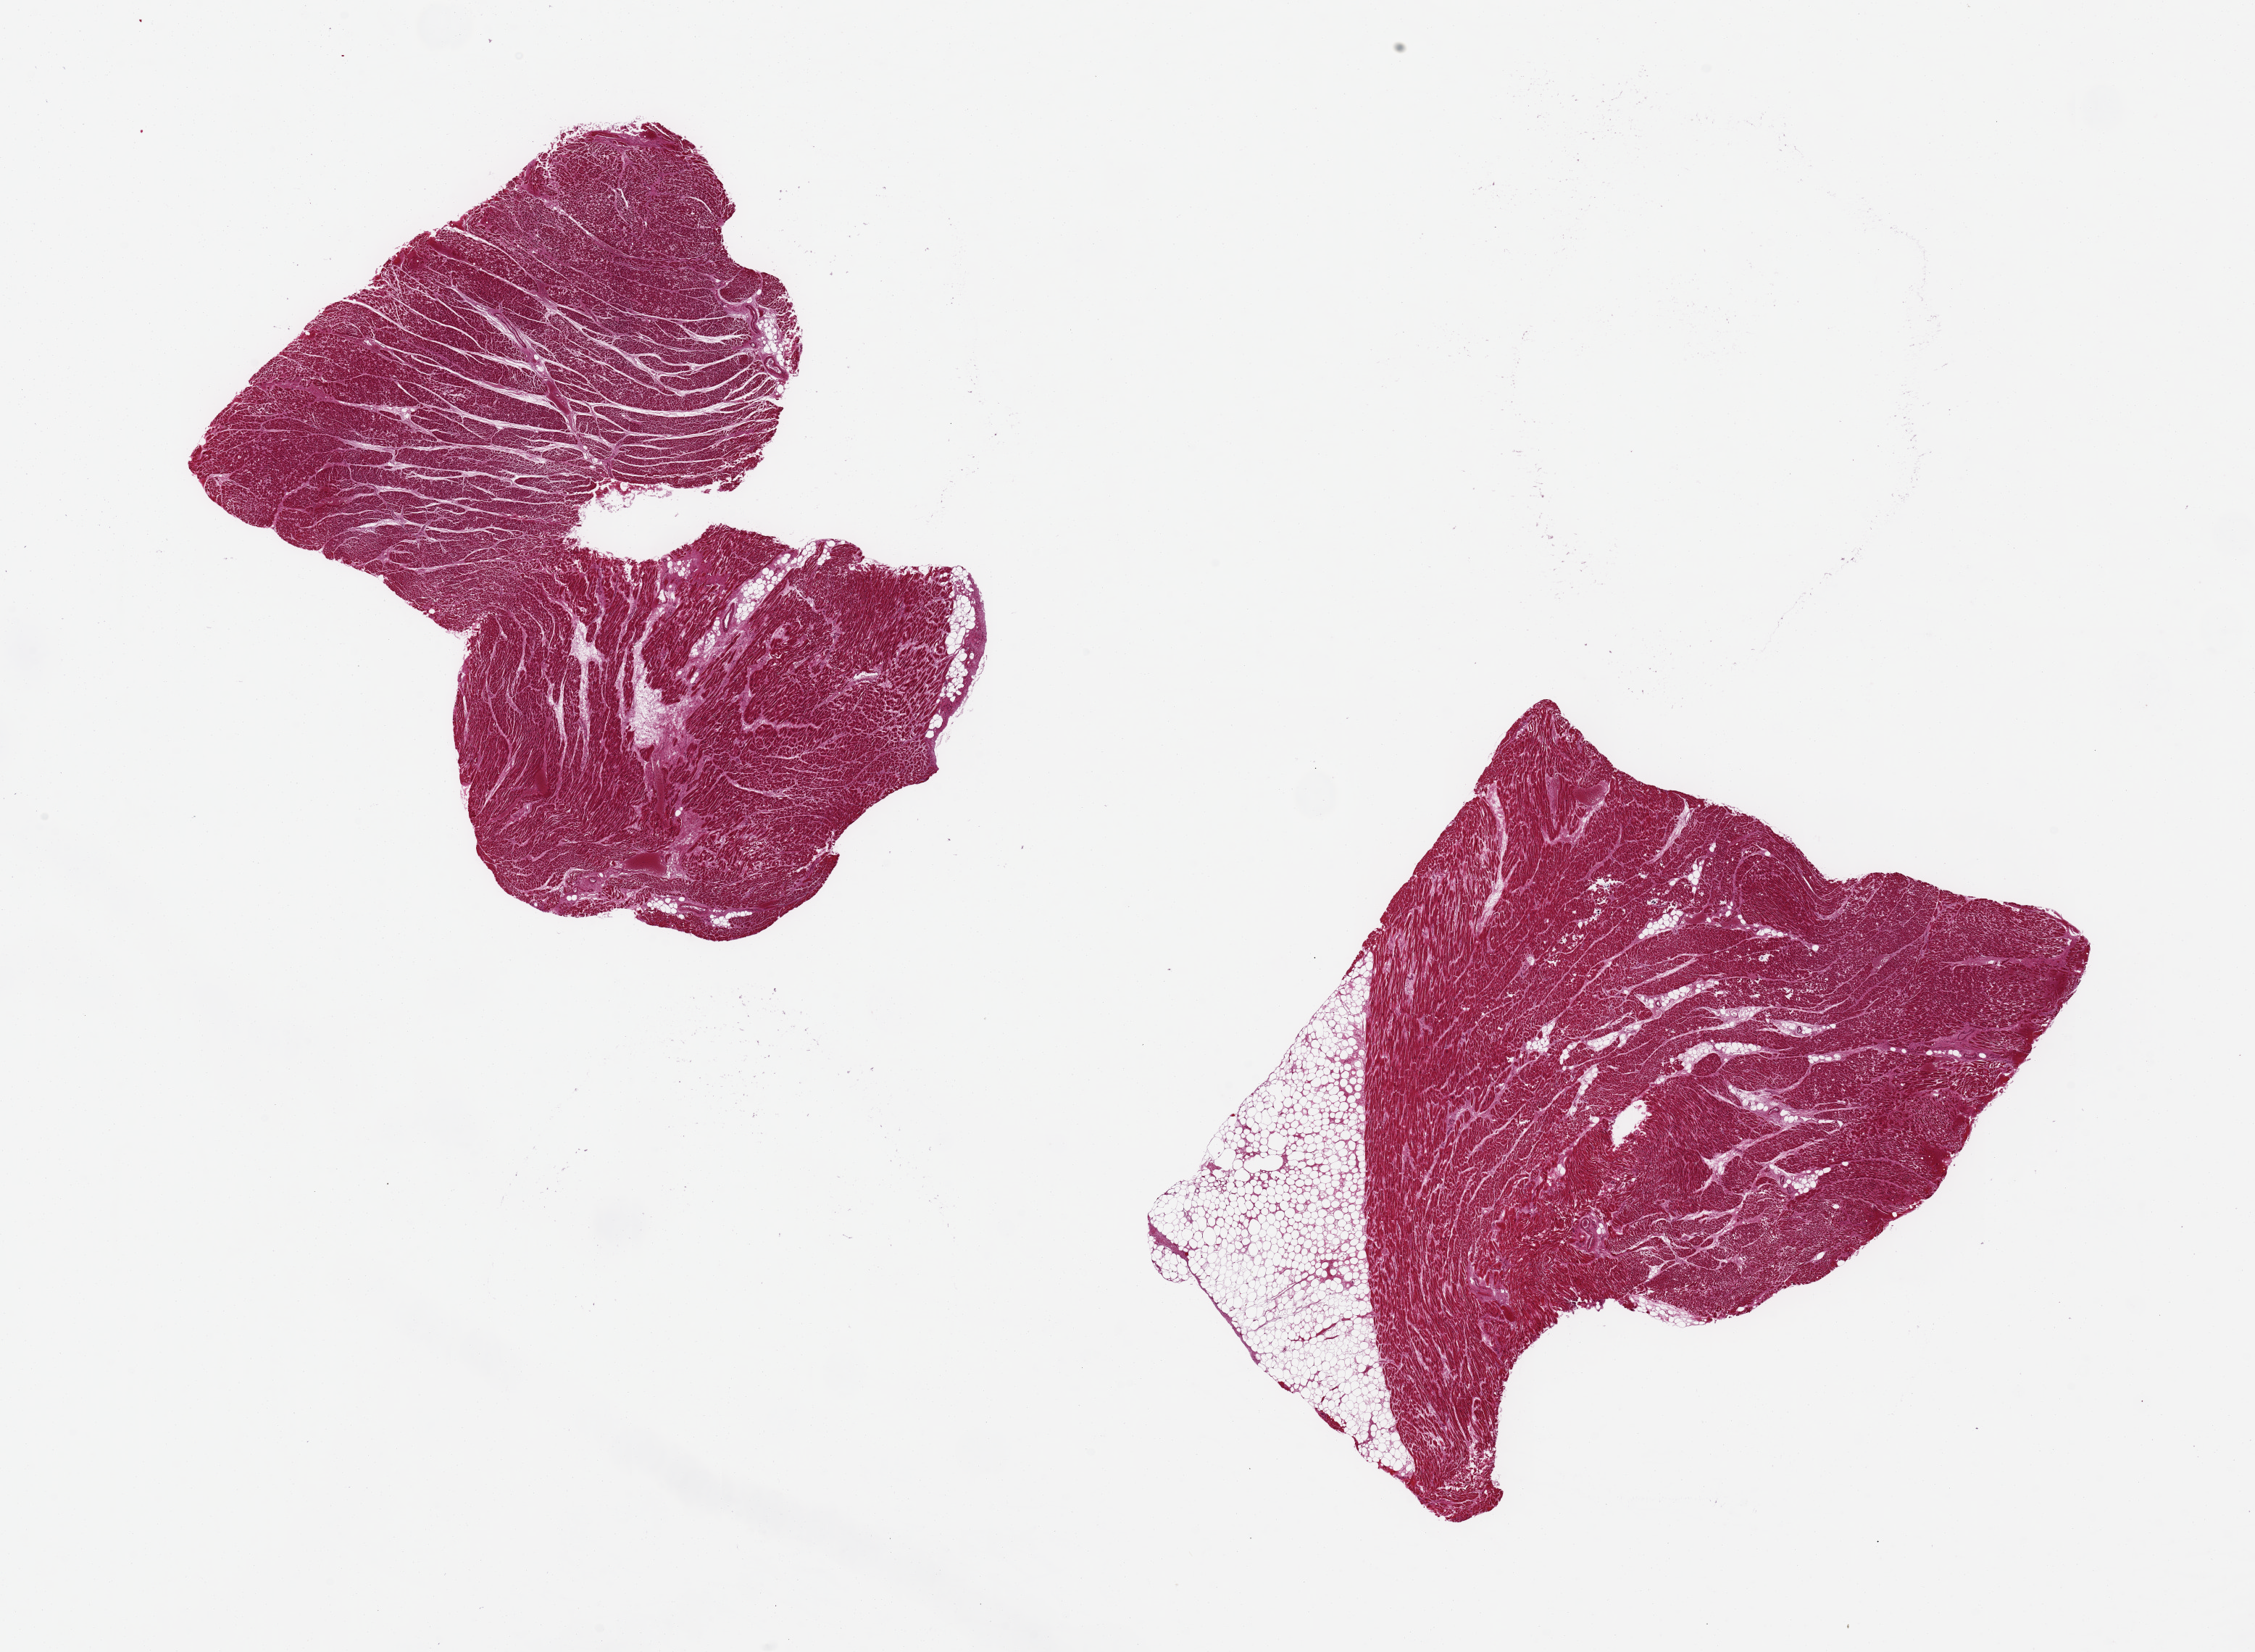
H&E whole-slide image, a low-resolution overview of the entire scanned area, about 24.6 x 18.0 mm (from a 20x scan). Donor sex: male.
• specimen: PAXgene-fixed, paraffin-embedded tissue; sampled site (target tissue): heart; donor tissue sample